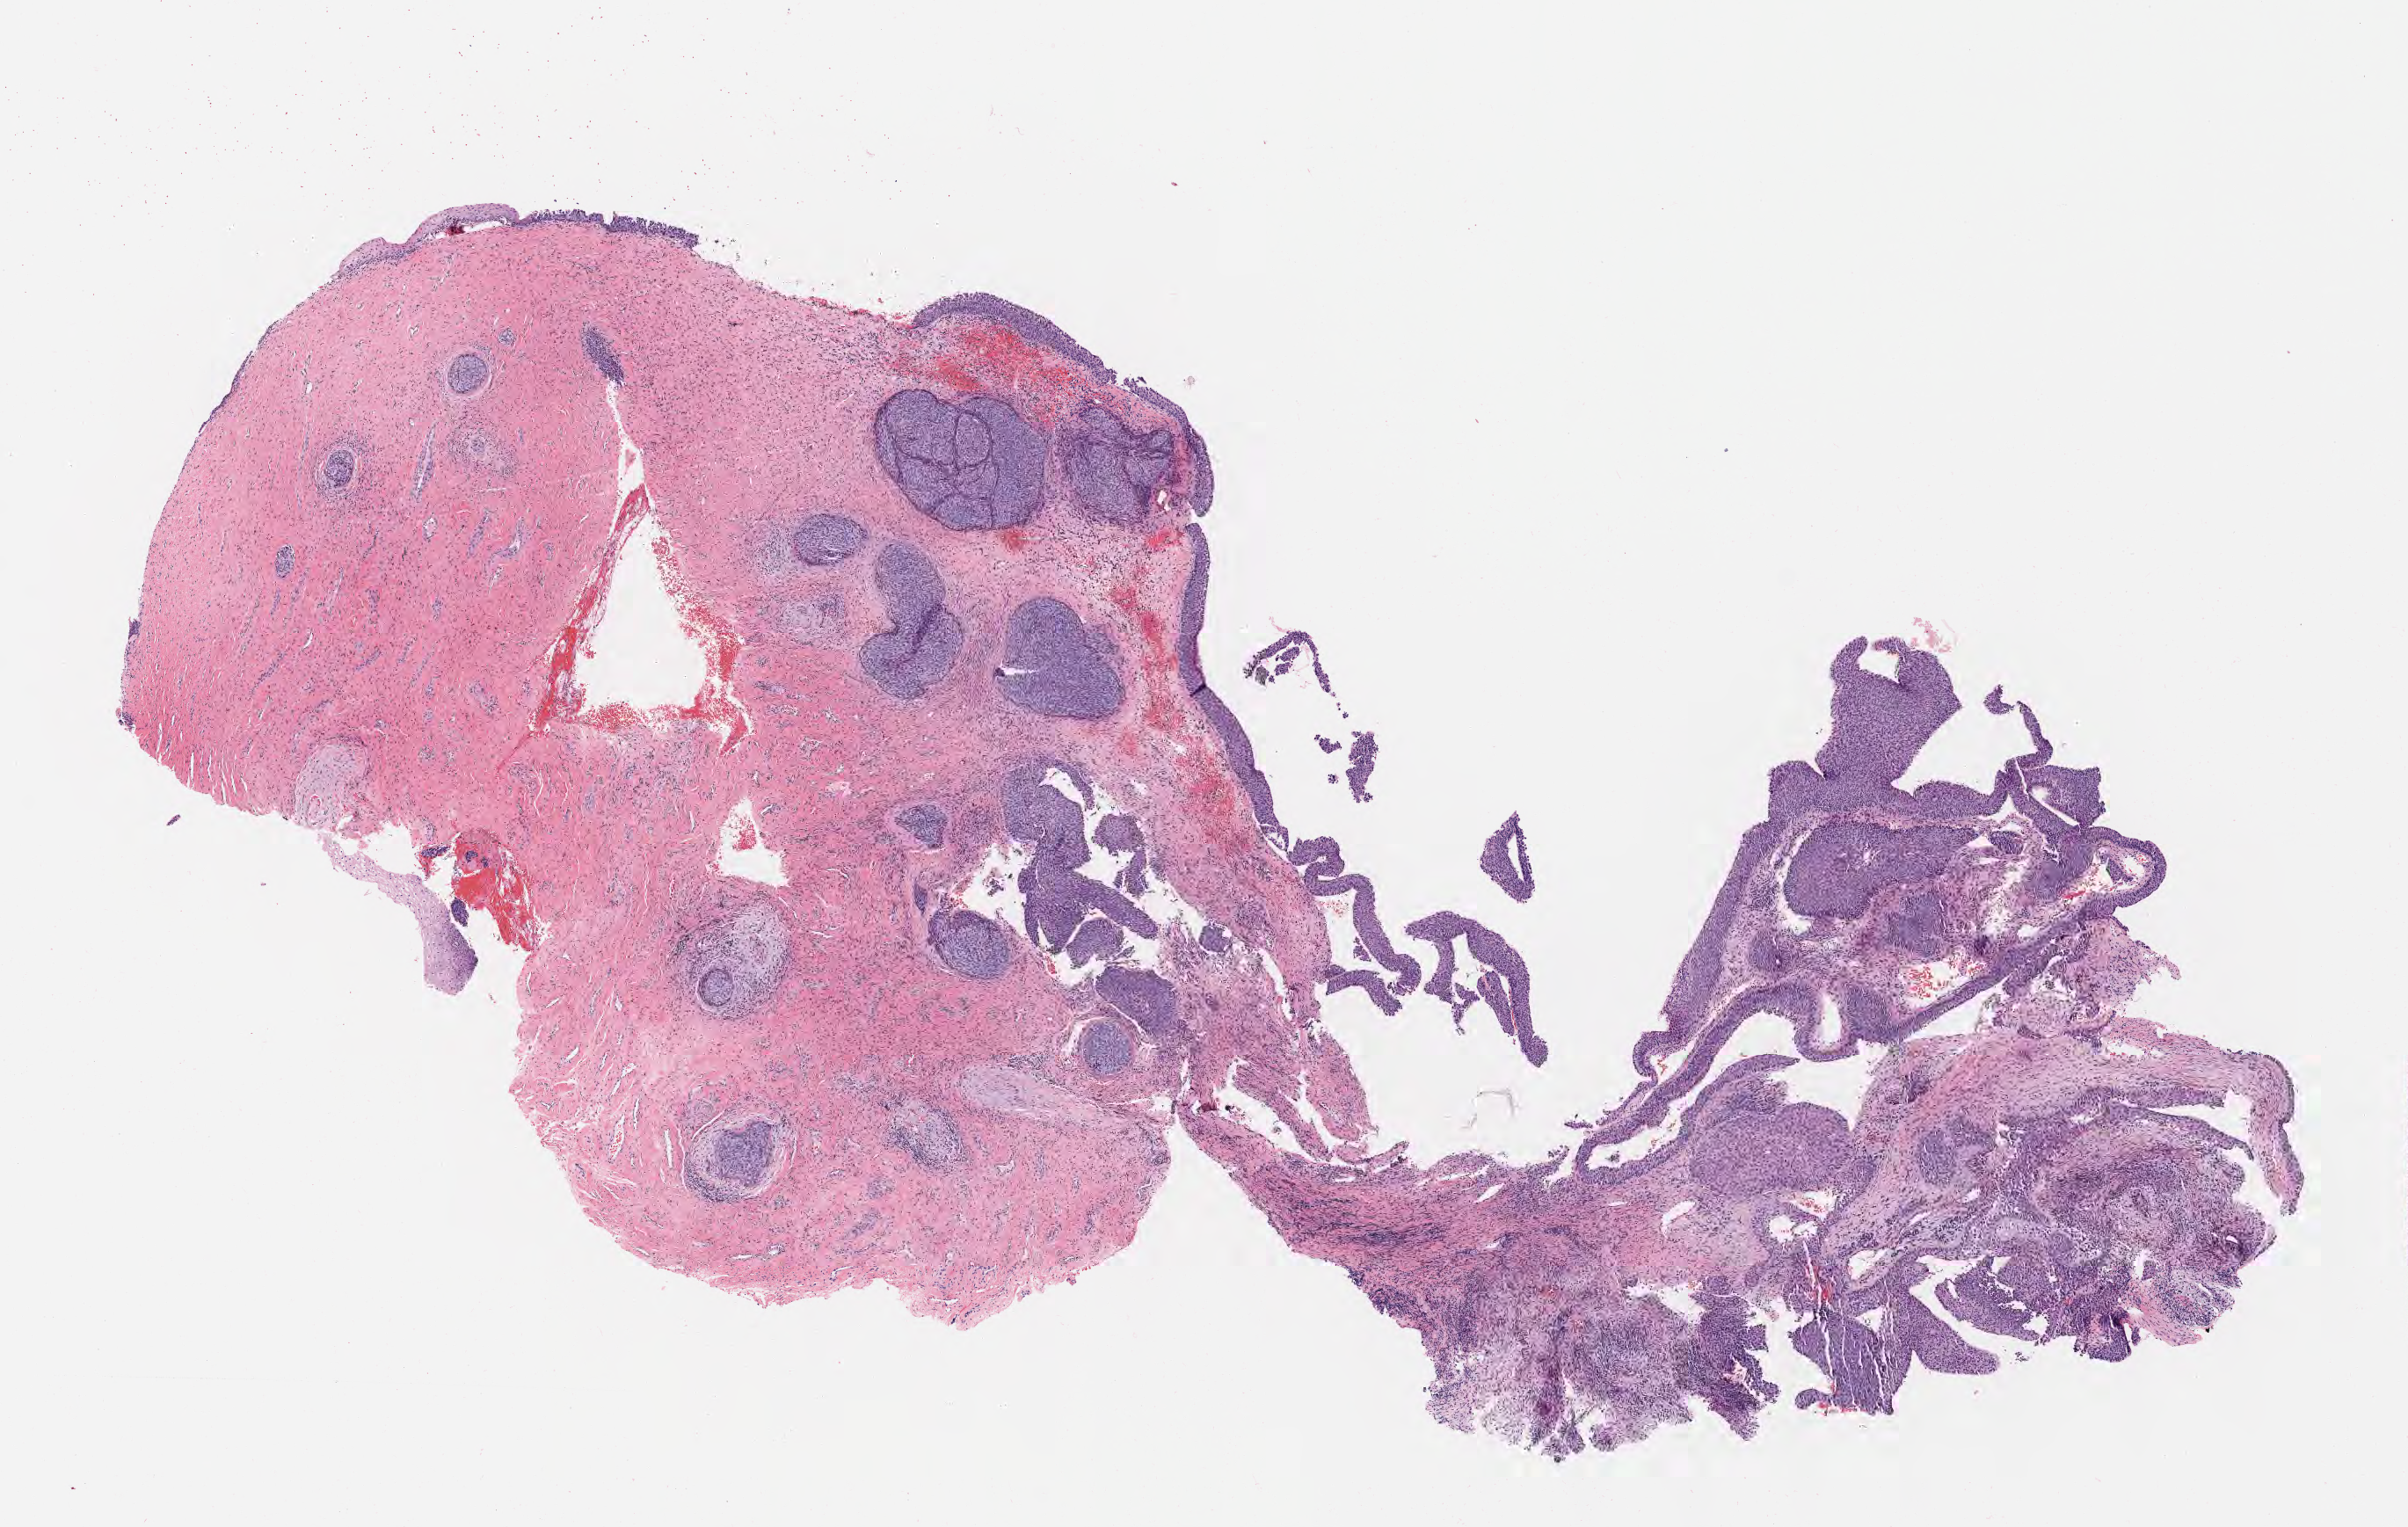
H&E whole-slide image, shown as a low-resolution overview of the whole scanned area (about 11.1 x 7.0 mm), specimen: tumor tissue, anatomic site: cervix. Female patient, age 54 years.
Histologic diagnosis: Squamous cell carcinoma, large cell, nonkeratinizing, NOS.